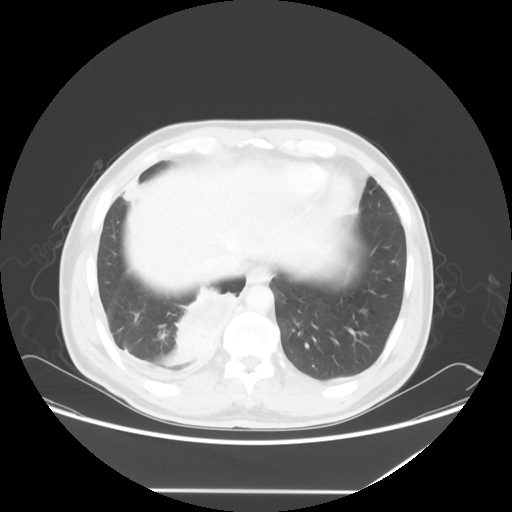
Chest CT, one axial slice; reconstruction kernel STANDARD; 120 kVp; lung window (W 1500 / L -600 HU); 5 mm slice thickness; 512 × 512 image matrix, field of view 419 × 419 mm. Male patient, age 48 years. From the clinical record (not read from this slice): clinical TNM (as recorded): T3 N3 M1a.
Outlined on this slice (rectangle marked by the reading radiologist):
- lung tumour (recorded histology: squamous cell carcinoma): bounding box (x1, y1, x2, y2) in pixels: (172, 278, 238, 361)